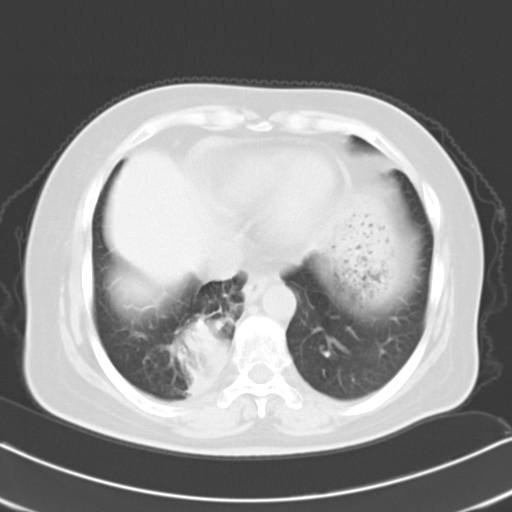
Chest CT, one axial slice. Slice 5 of 21 in the series (ordered by position). 120 kVp. Lung window (W 1500 / L -600 HU). 10 mm slice thickness. 512 × 512 image matrix, field of view 326 × 326 mm. Female patient, age 61 years. From the clinical record (not read from this slice): clinical TNM (as recorded): T1b N0 M1b.
Structures marked on this image (rectangle marked by the reading radiologist):
- lung tumour (recorded histology: squamous cell carcinoma): bounding box <161,300,233,415> (left, top, right, bottom; pixels)